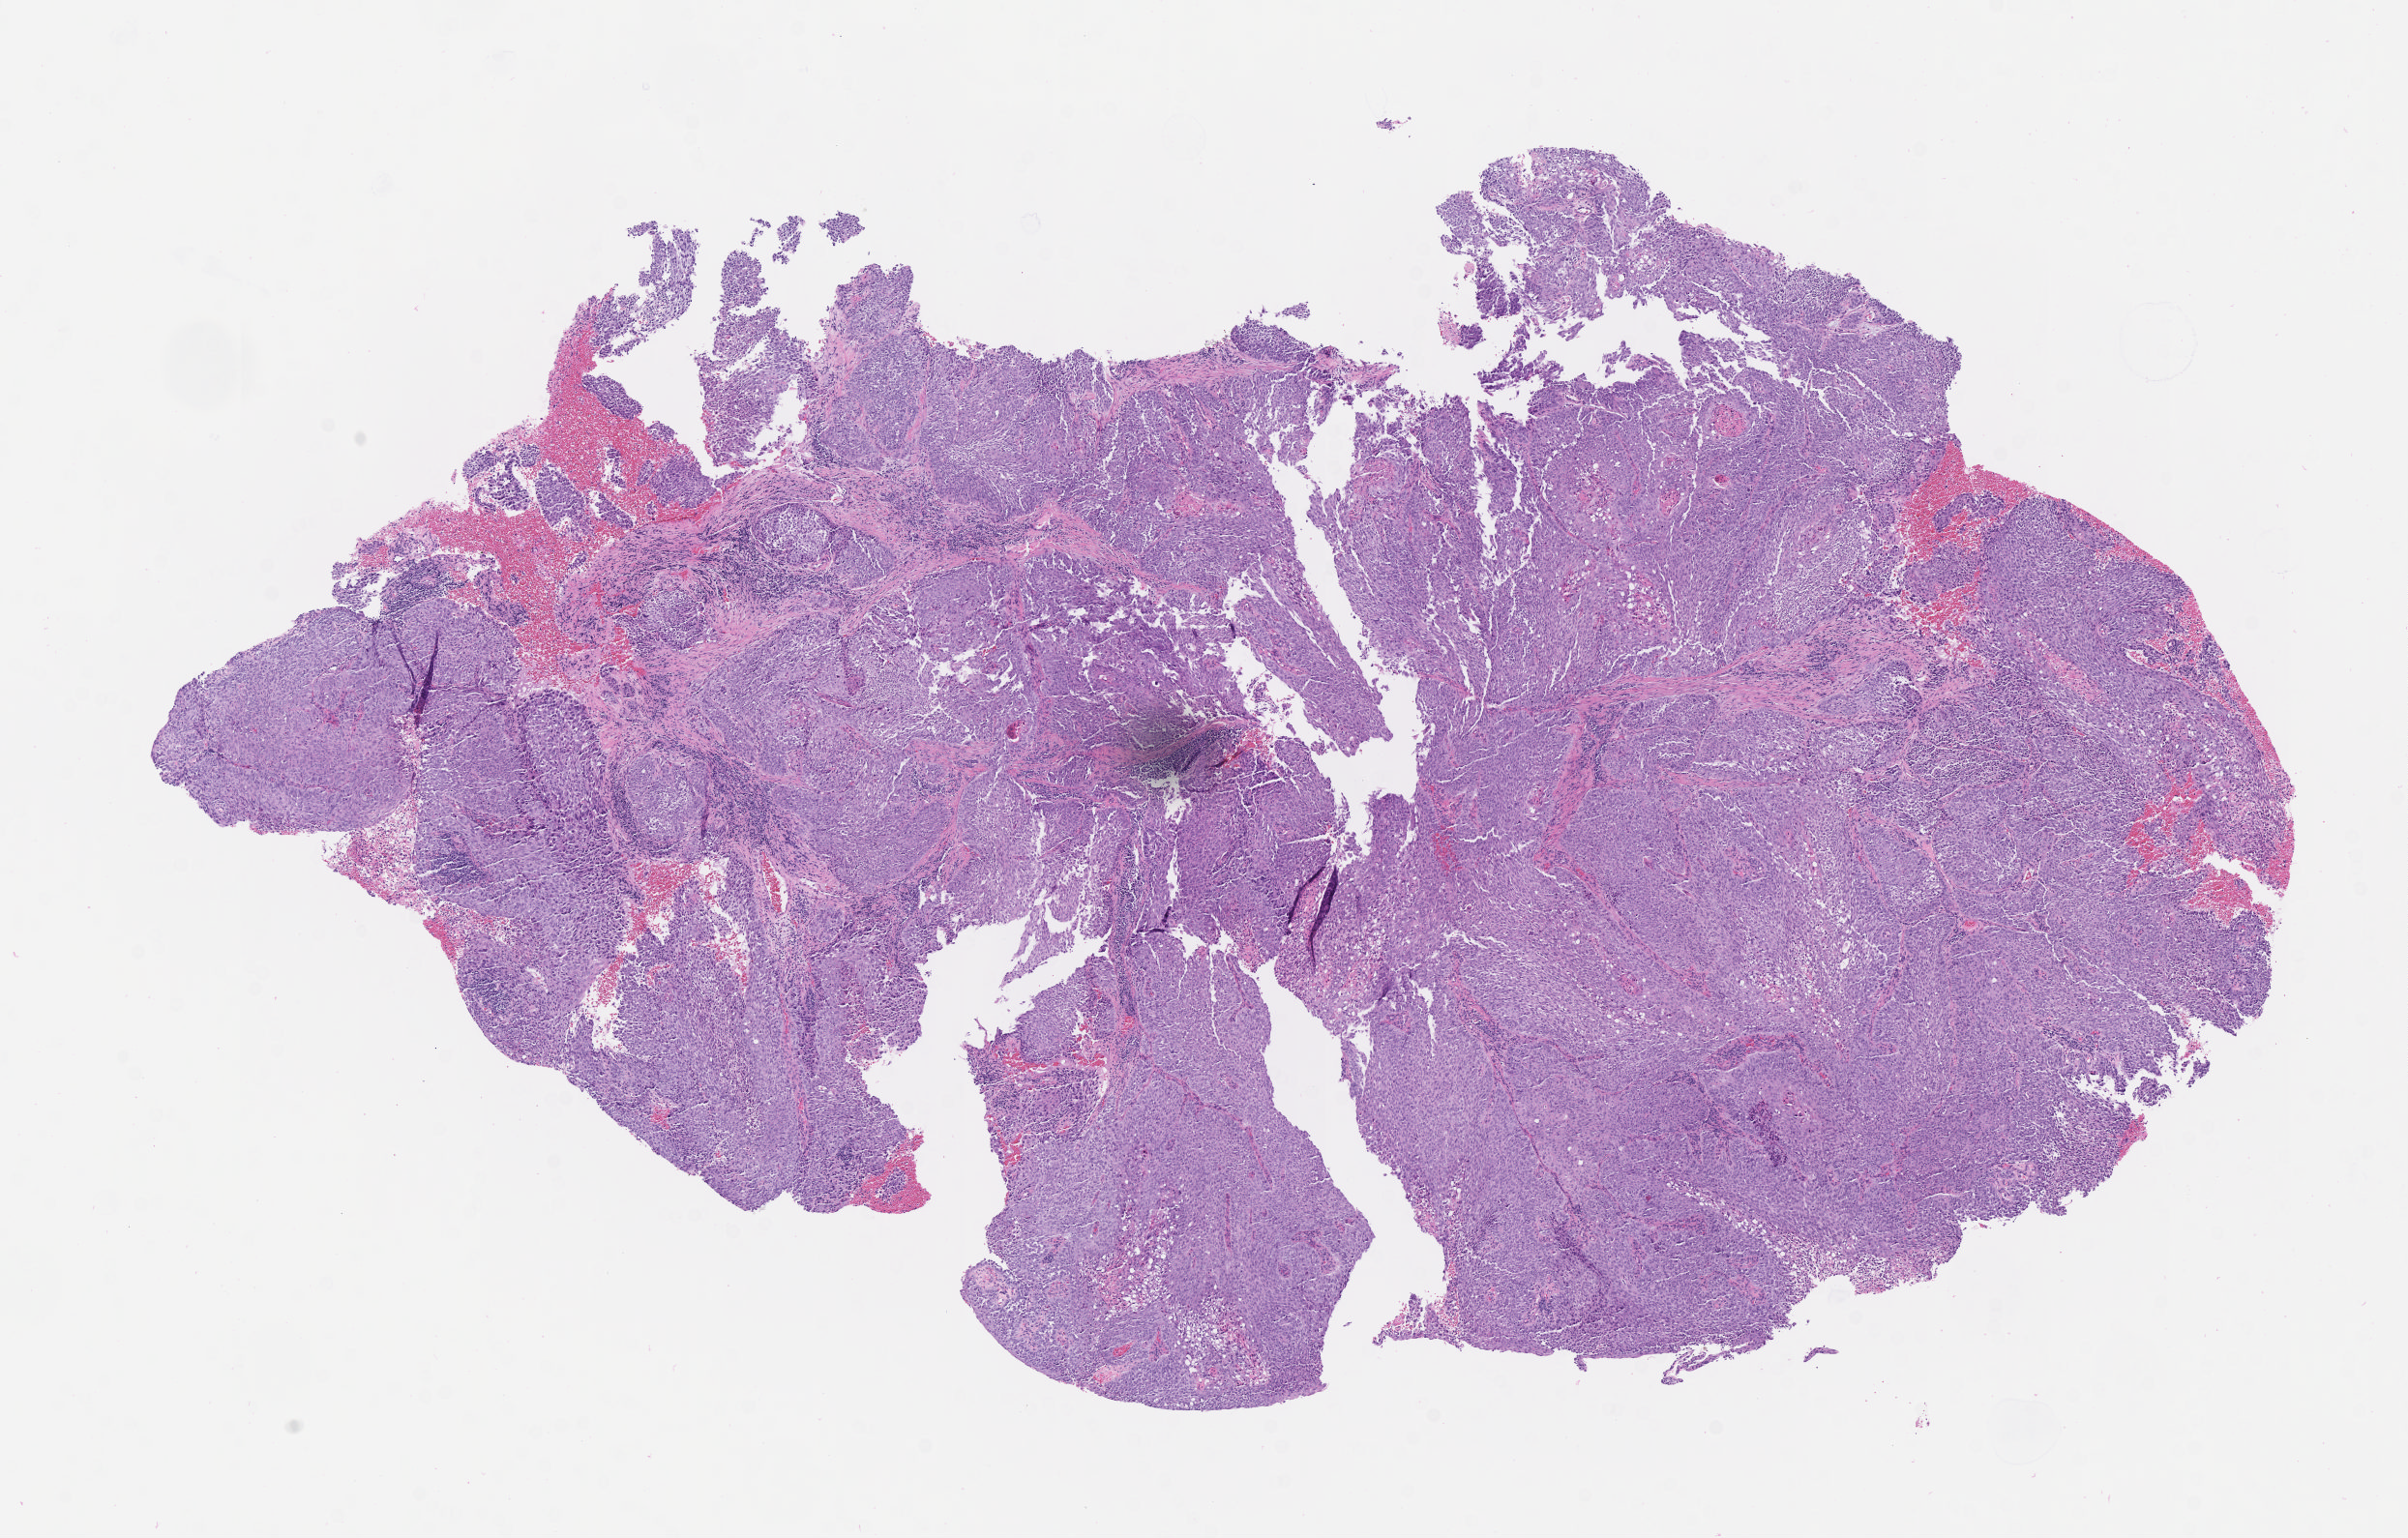
Digitized H&E-stained section, shown as a low-resolution overview of the whole scanned area (about 10.1 x 6.4 mm), specimen: tumor tissue, anatomic site: cervix. Patient: female, 45 years old.
* histologic diagnosis: Squamous cell carcinoma, keratinizing, NOS